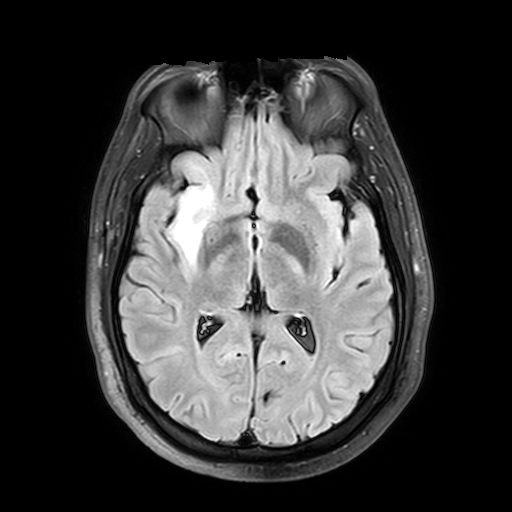
Brain MRI from a brain-tumour surgery series, one axial slice. Position 22 of 42 along the scan axis. T2 FLAIR. 4 mm slice thickness. 512 × 512 image matrix, field of view 240 × 240 mm. From the clinical record (not read from this slice): histopathology: Astrocytoma; WHO grade: 2; IDH mutation: yes.
Structures marked on this image (manually delineated by an expert):
- tumour: bounding box (x1, y1, x2, y2) in pixels: (137, 186, 223, 262)